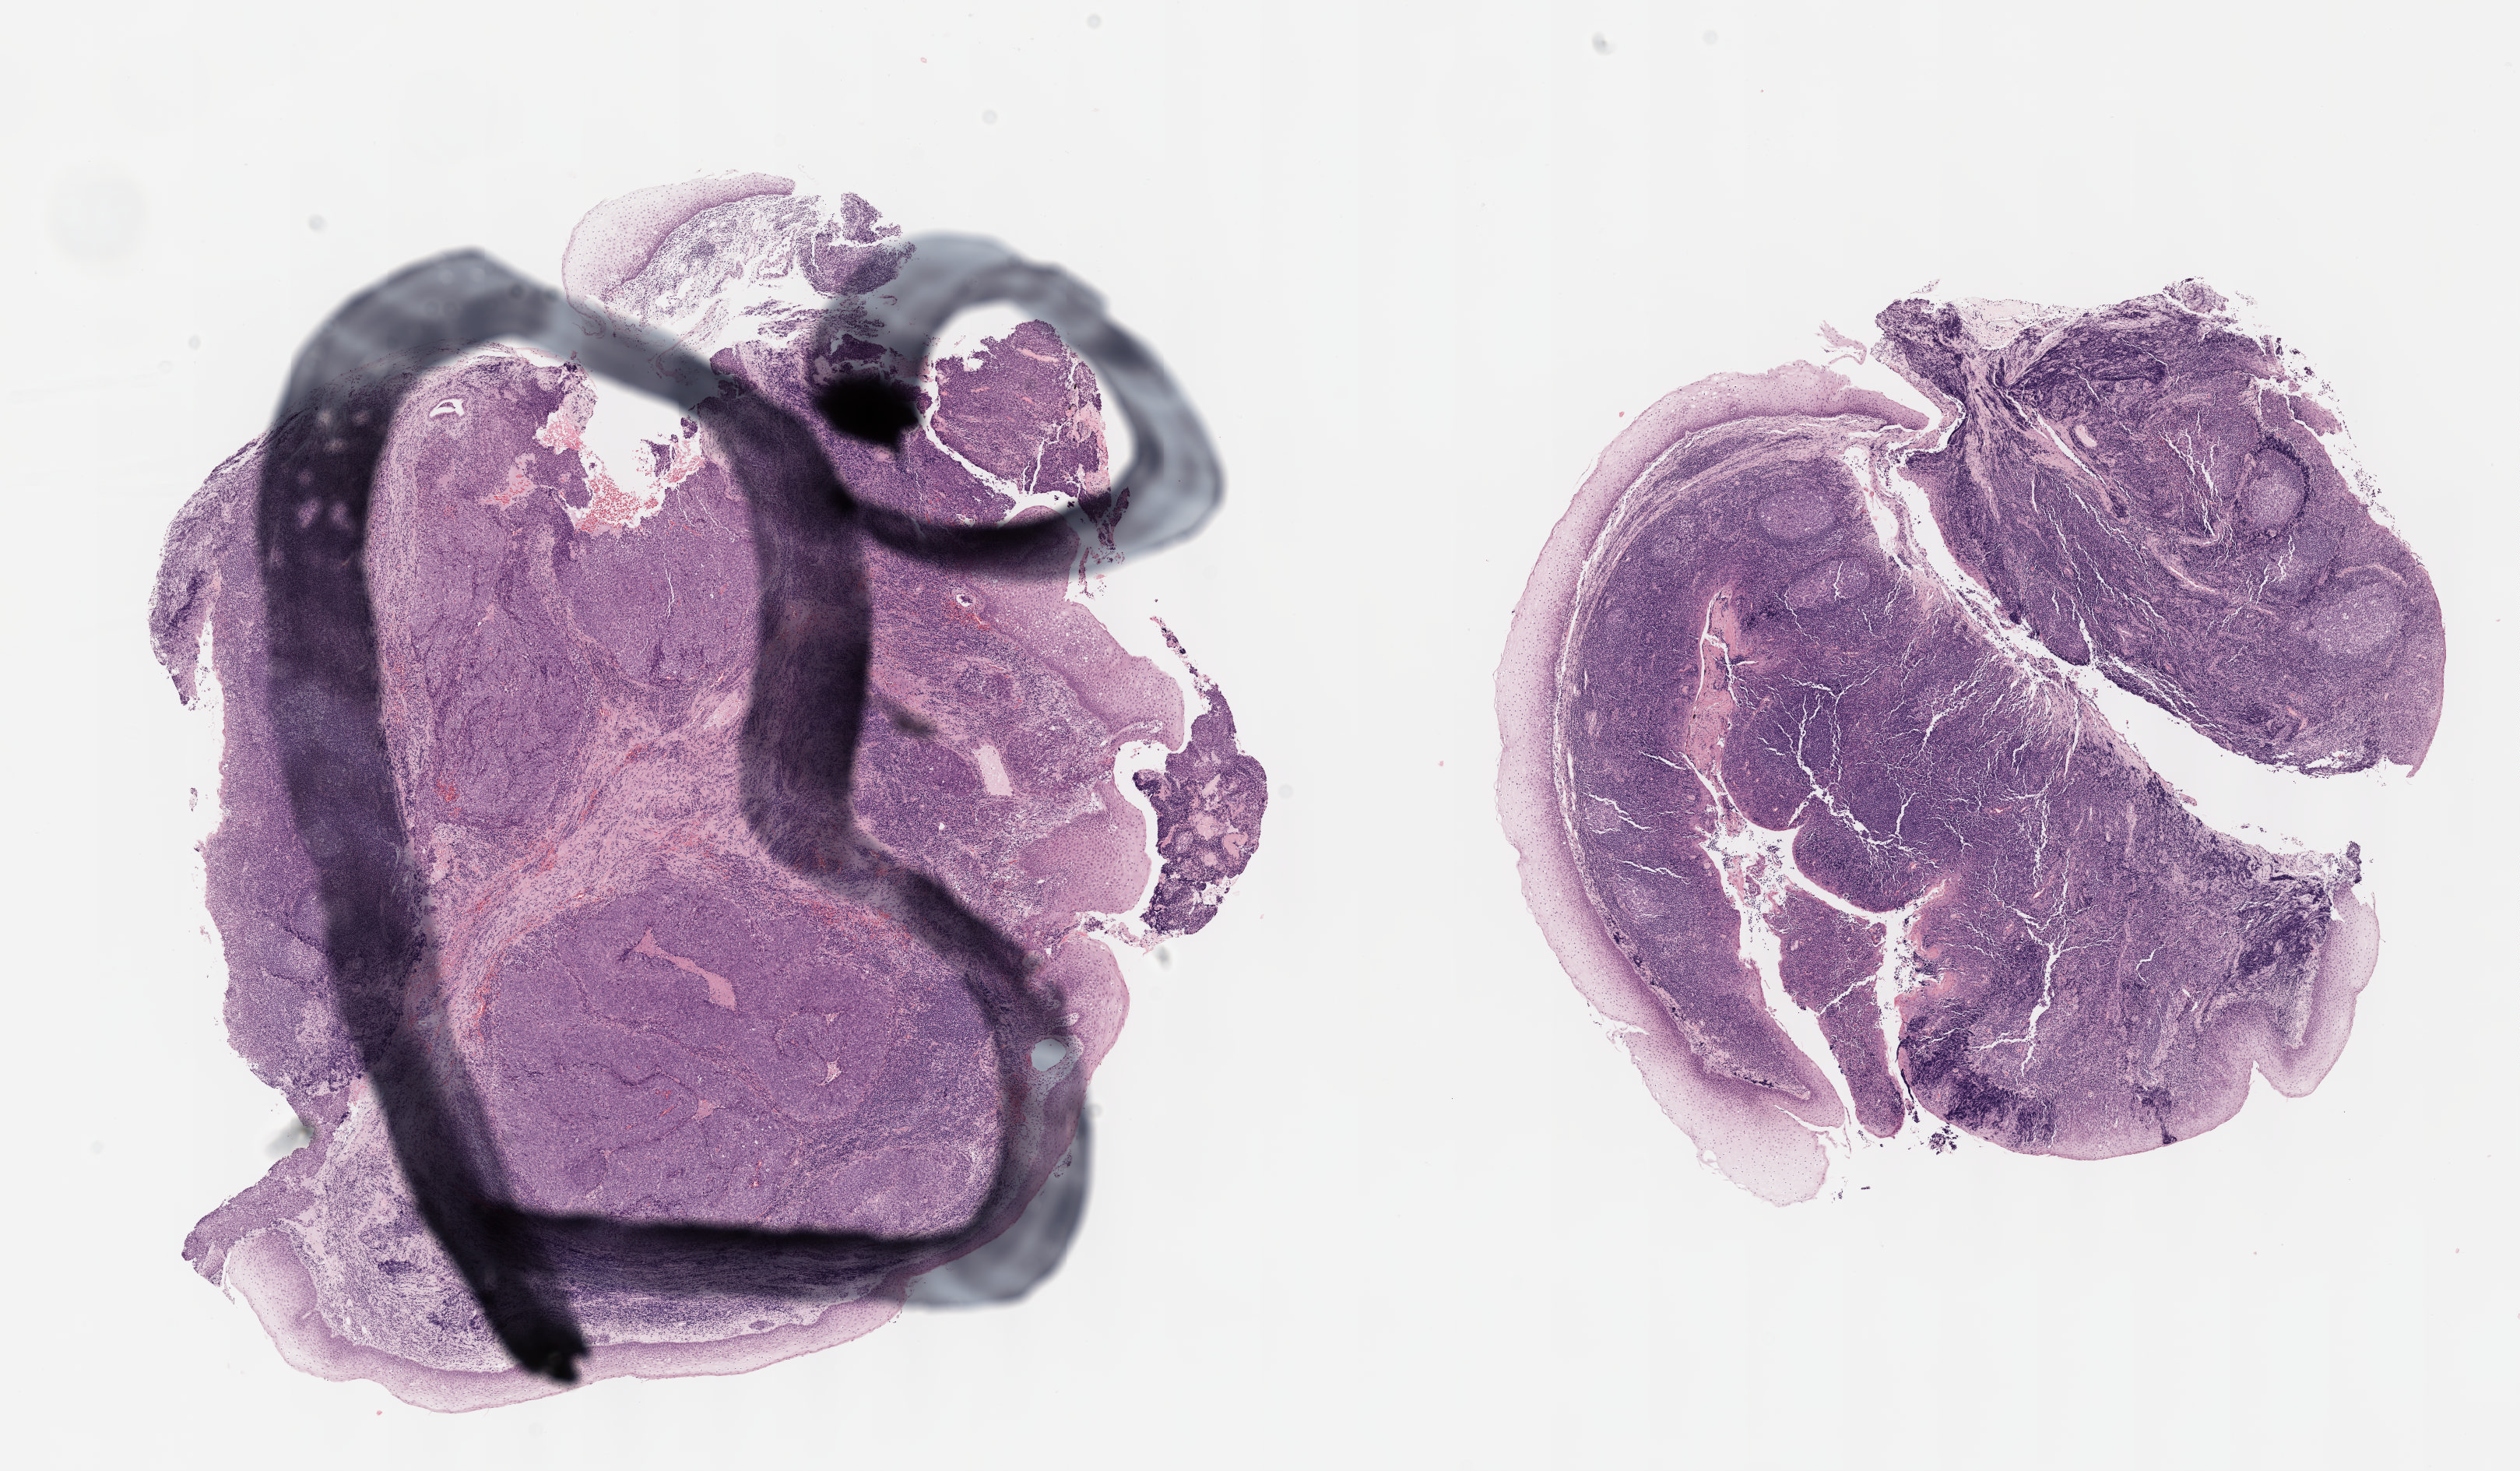
Digitized Hematoxylin and eosin (H&E) stained tissue section (whole slide), whole scanned area (about 13.1 x 7.6 mm) shown as a low-resolution overview; FFPE section; sample: primary tumour, head and neck. Male patient; age at initial diagnosis 62 years. Histologic grade: G4 (undifferentiated).
• pathologic diagnosis: Squamous cell carcinoma, NOS (base of tongue, NOS)